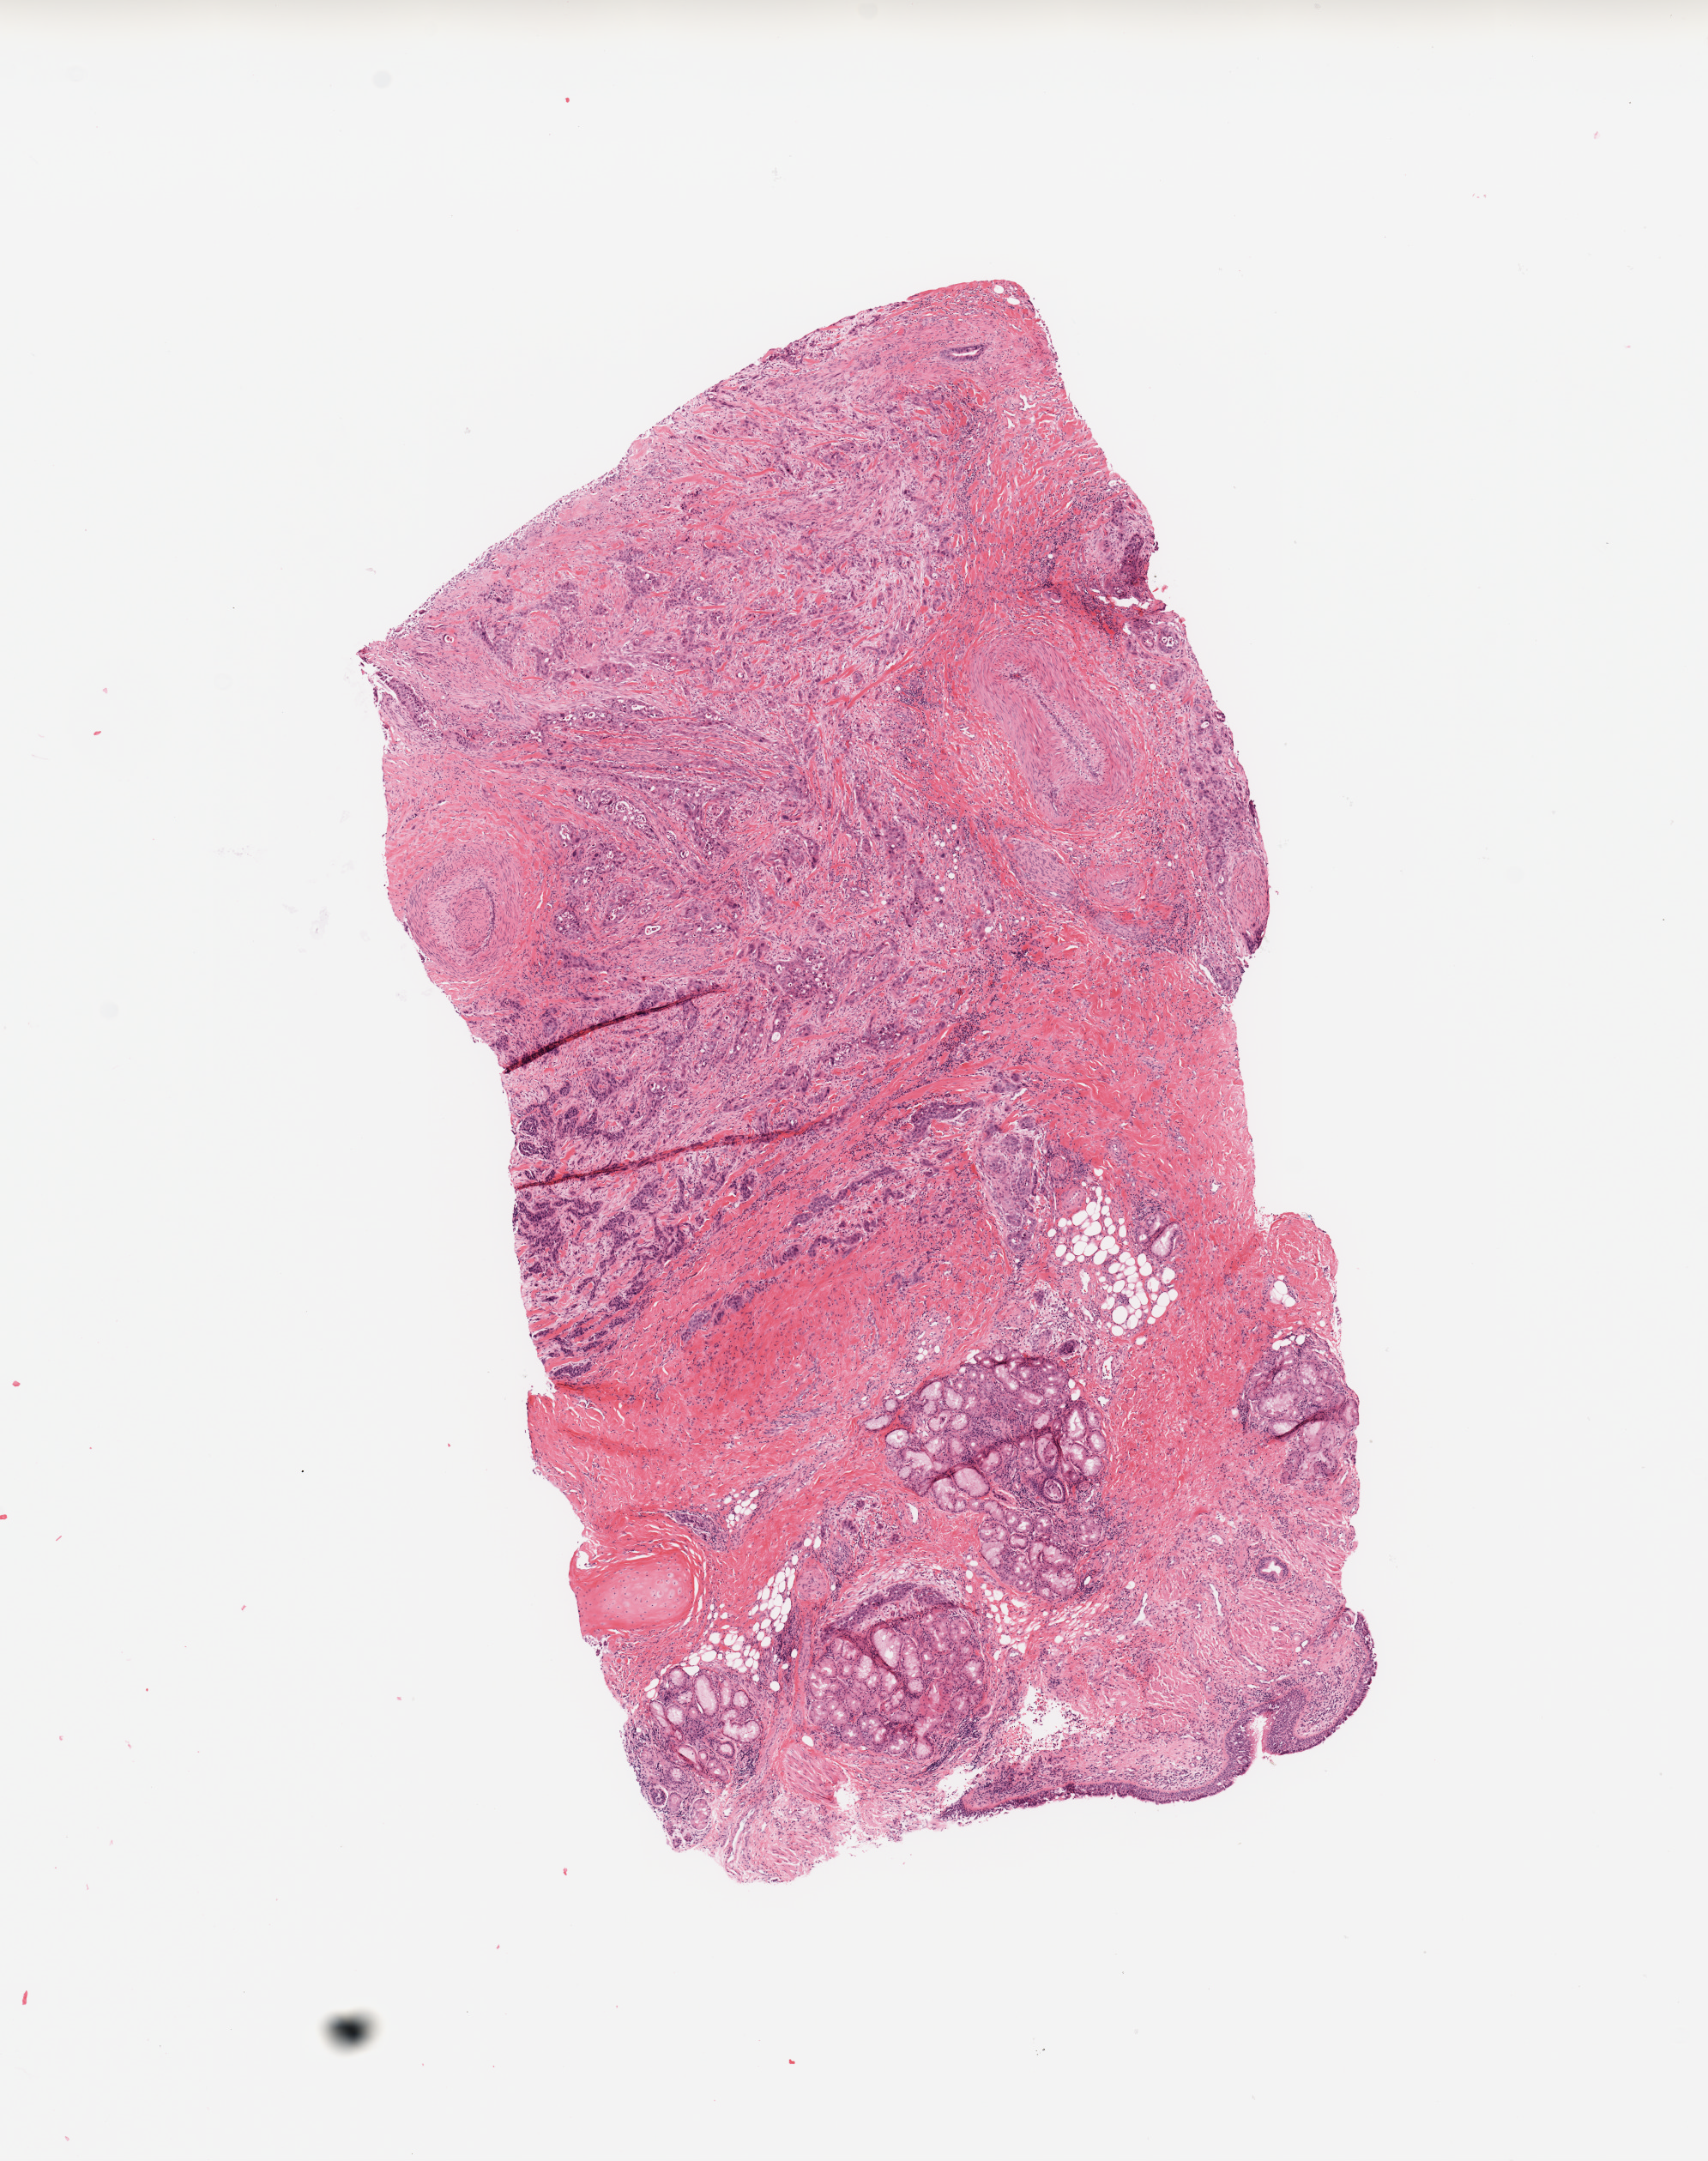
Digitized Hematoxylin and eosin (H&E) stained tissue section (whole slide), whole scanned area (about 7.9 x 10.0 mm, from a 20x scan) shown as a low-resolution overview. Lung, tumour tissue. Patient: male, age 40 years. Histologic grade: G3 (poorly differentiated).
Diagnosis: Squamous cell carcinoma, NOS. Primary tumour site (as recorded): right middle lobe. AJCC pathologic stage: IIIA.